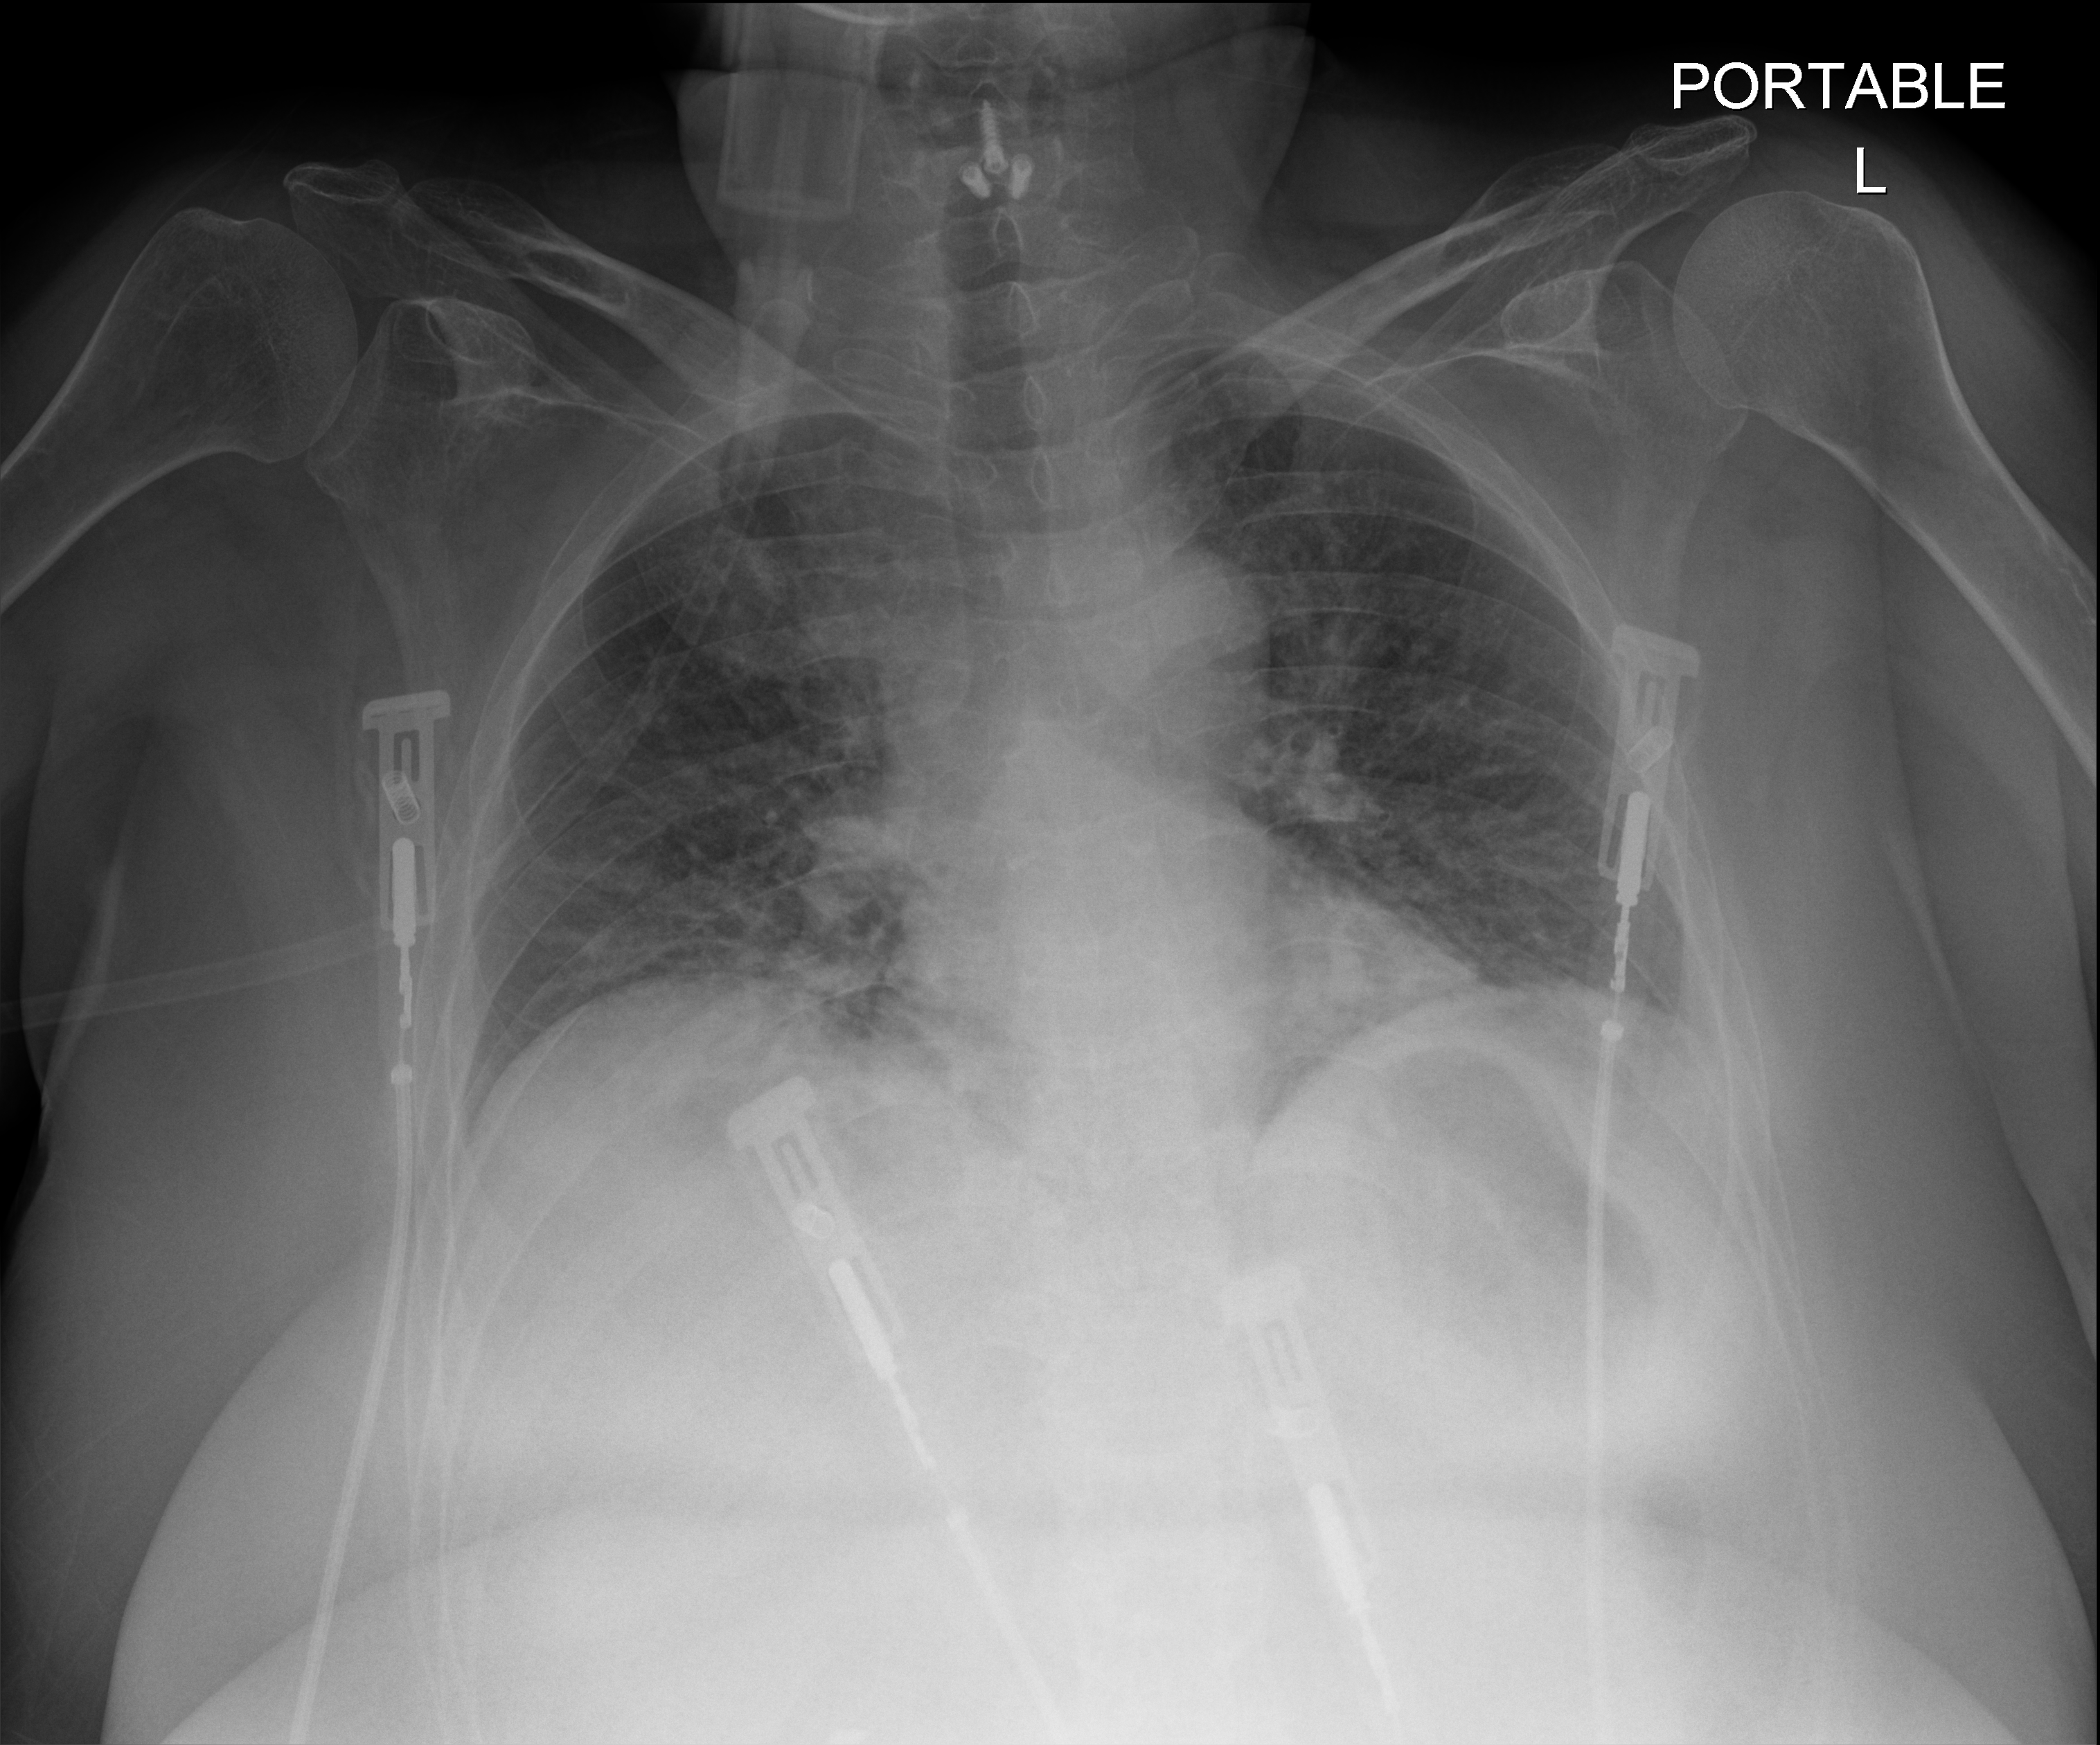
Chest radiograph; anteroposterior (AP) projection. Female patient hospitalised with COVID-19, age 18–59 years.
Admission-level facts for this patient (not findings on this image; timing relative to this image not recorded): mechanically ventilated during this hospital stay: no; length of hospital stay: 44 days; admitted to intensive care during this hospital stay: yes.